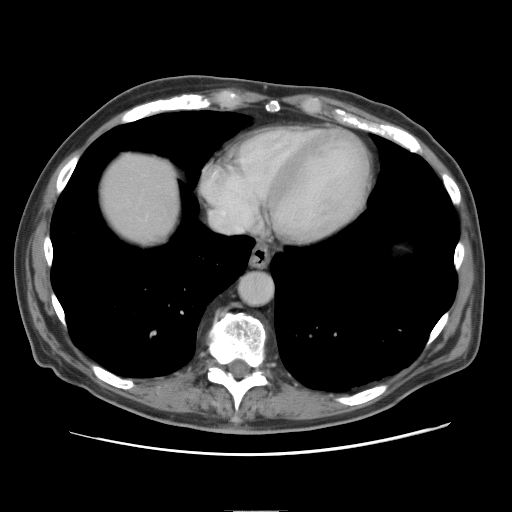
Contrast-enhanced abdominal CT, one axial slice. 120 kVp. Intravenous contrast given. Soft-tissue window (W 400 / L 40 HU). 512 × 512 image matrix, field of view 375 × 375 mm. Male patient, age 69 years. Case-level facts recorded for this patient, not image findings: diagnosis: colorectal cancer liver metastases, imaged before liver resection; multiple liver metastases: no; largest metastasis: 8.5 cm; disease in both lobes: no.
Structures marked on this image (manually delineated by an expert):
- liver: box from (x=101, y=152) to (x=179, y=245) px
- planned liver remnant (the part of the liver to remain after resection): (x=101, y=152)–(x=180, y=245)